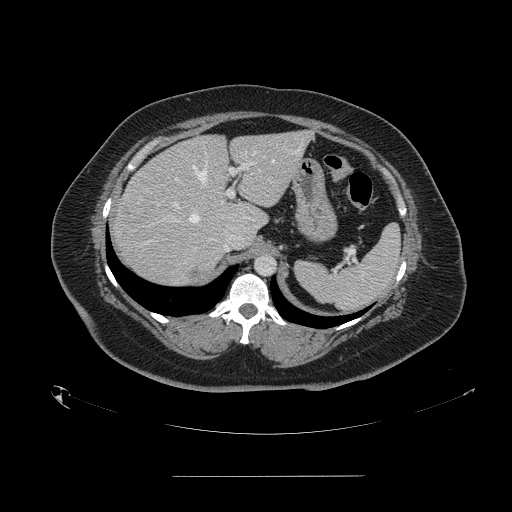
Contrast-enhanced abdominal CT, one axial slice. Position 108 of 164 along the scan axis. 120 kVp. Intravenous contrast given. Soft-tissue window (W 400 / L 40 HU). 2.5 mm slice thickness. 512 × 512 image matrix, field of view 495 × 495 mm. Female patient, age 52 years. From the clinical record (not read from this slice): diagnosis: colorectal cancer liver metastases, imaged before liver resection; multiple liver metastases: yes; largest metastasis: 3.5 cm; chemotherapy before resection: no.
Structures marked on this image (expert manual segmentation):
- hepatic veins: bounding box [x1, y1, x2, y2] px = [189, 148, 300, 223]
- liver: [113, 132, 310, 287]
- planned liver remnant (the part of the liver to remain after resection): [173, 132, 310, 231]
- portal vein (with intrahepatic branches): [172, 162, 252, 208]
- liver metastasis: [190, 268, 207, 278]
- liver metastasis: [250, 212, 260, 221]
- liver metastasis: [127, 209, 130, 215]